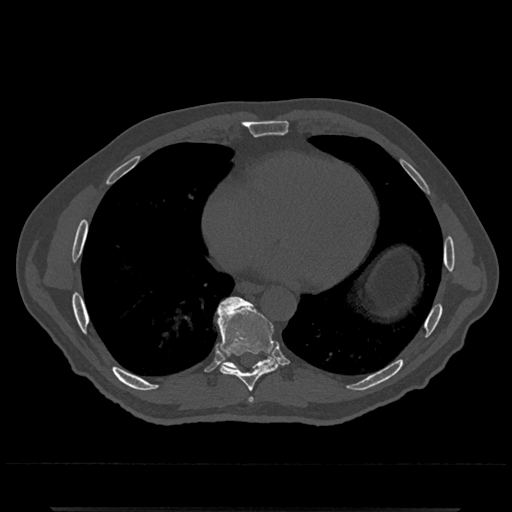
CT including the spine, one axial slice. Slice 652 of 797 in the series (ordered by position). Reconstruction kernel Br40s/3. Bone window (W 1800 / L 400 HU). 0.5 mm slice thickness. 512 × 512 image matrix. Male patient, age 67 years. From the clinical record (not read from this slice): primary cancer: prostate.
Outlined on this slice (semi-automatic segmentation, software-assisted and operator-edited):
- T7 vertebra: bounding box (x1, y1, x2, y2) in pixels: (249, 398, 253, 402)
- T8 vertebra: (216, 296, 280, 392)
- T9 vertebra: (215, 297, 278, 371)